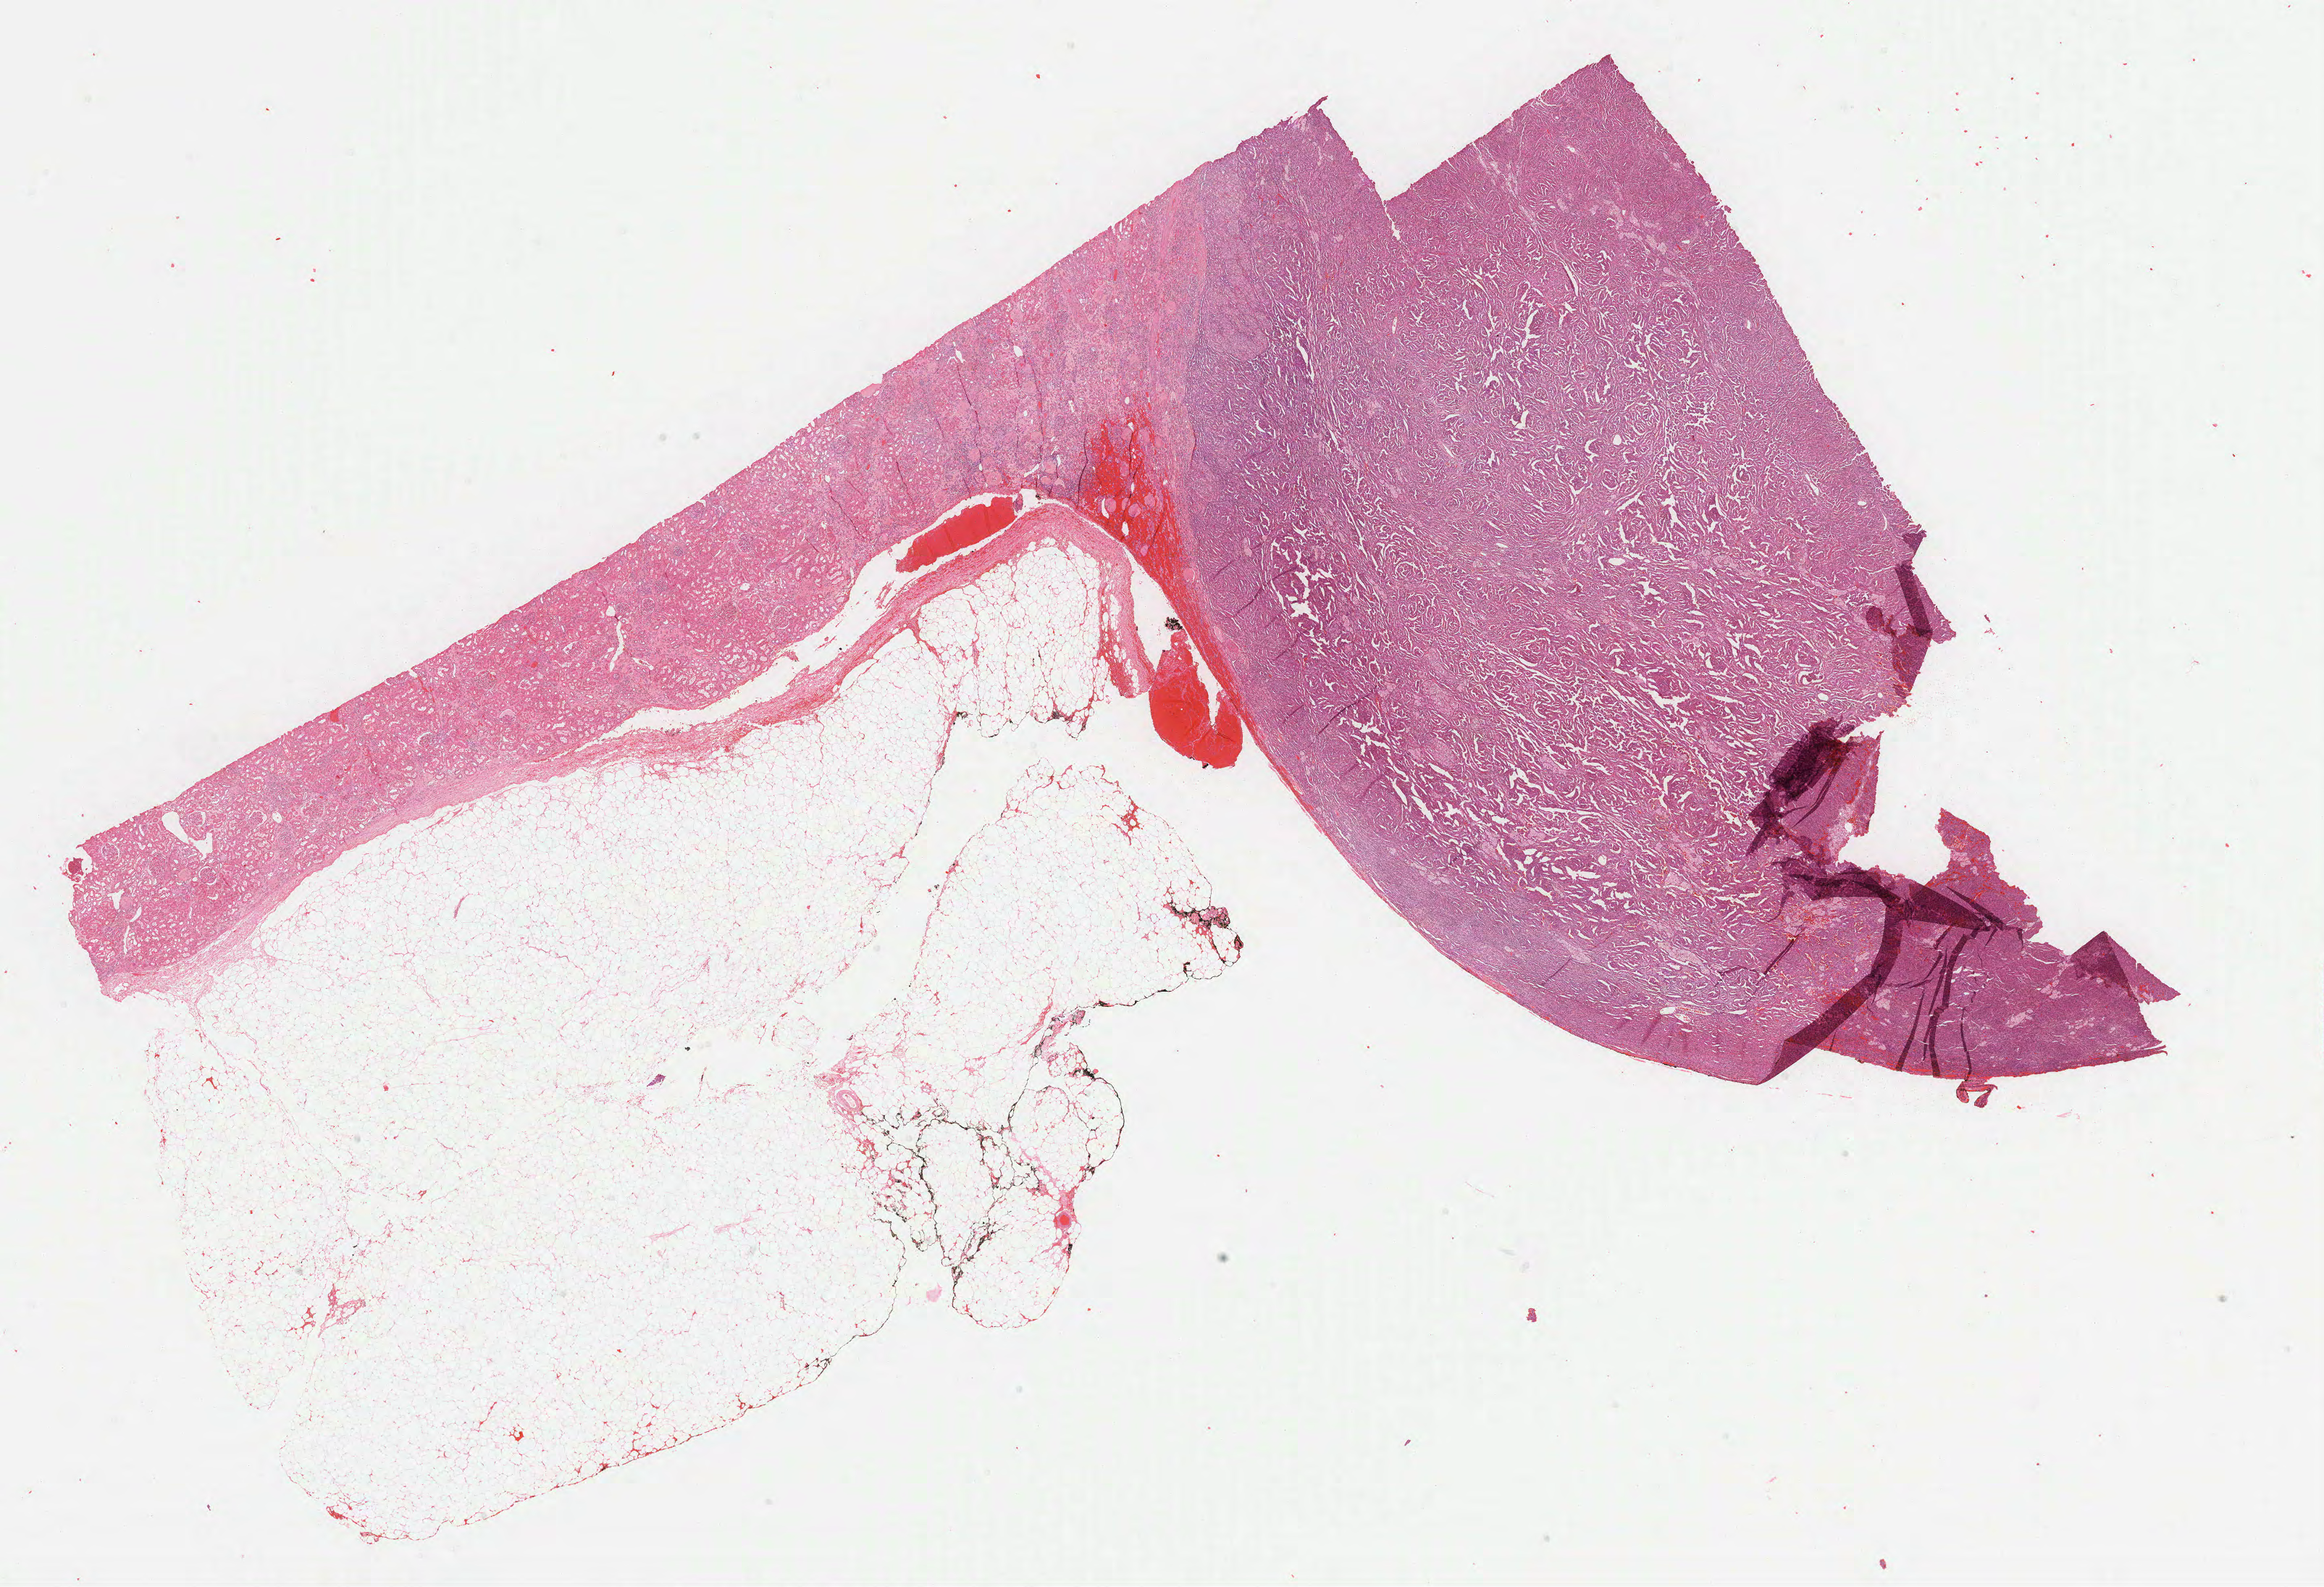
Whole-slide histology image, H&E — low-resolution overview of the scanned area, about 25.9 x 17.7 mm. Formalin-fixed paraffin-embedded (FFPE) diagnostic section. Sample: primary tumour, kidney. Male patient; age at initial diagnosis 66 years.
Histologic diagnosis: Papillary adenocarcinoma, NOS.